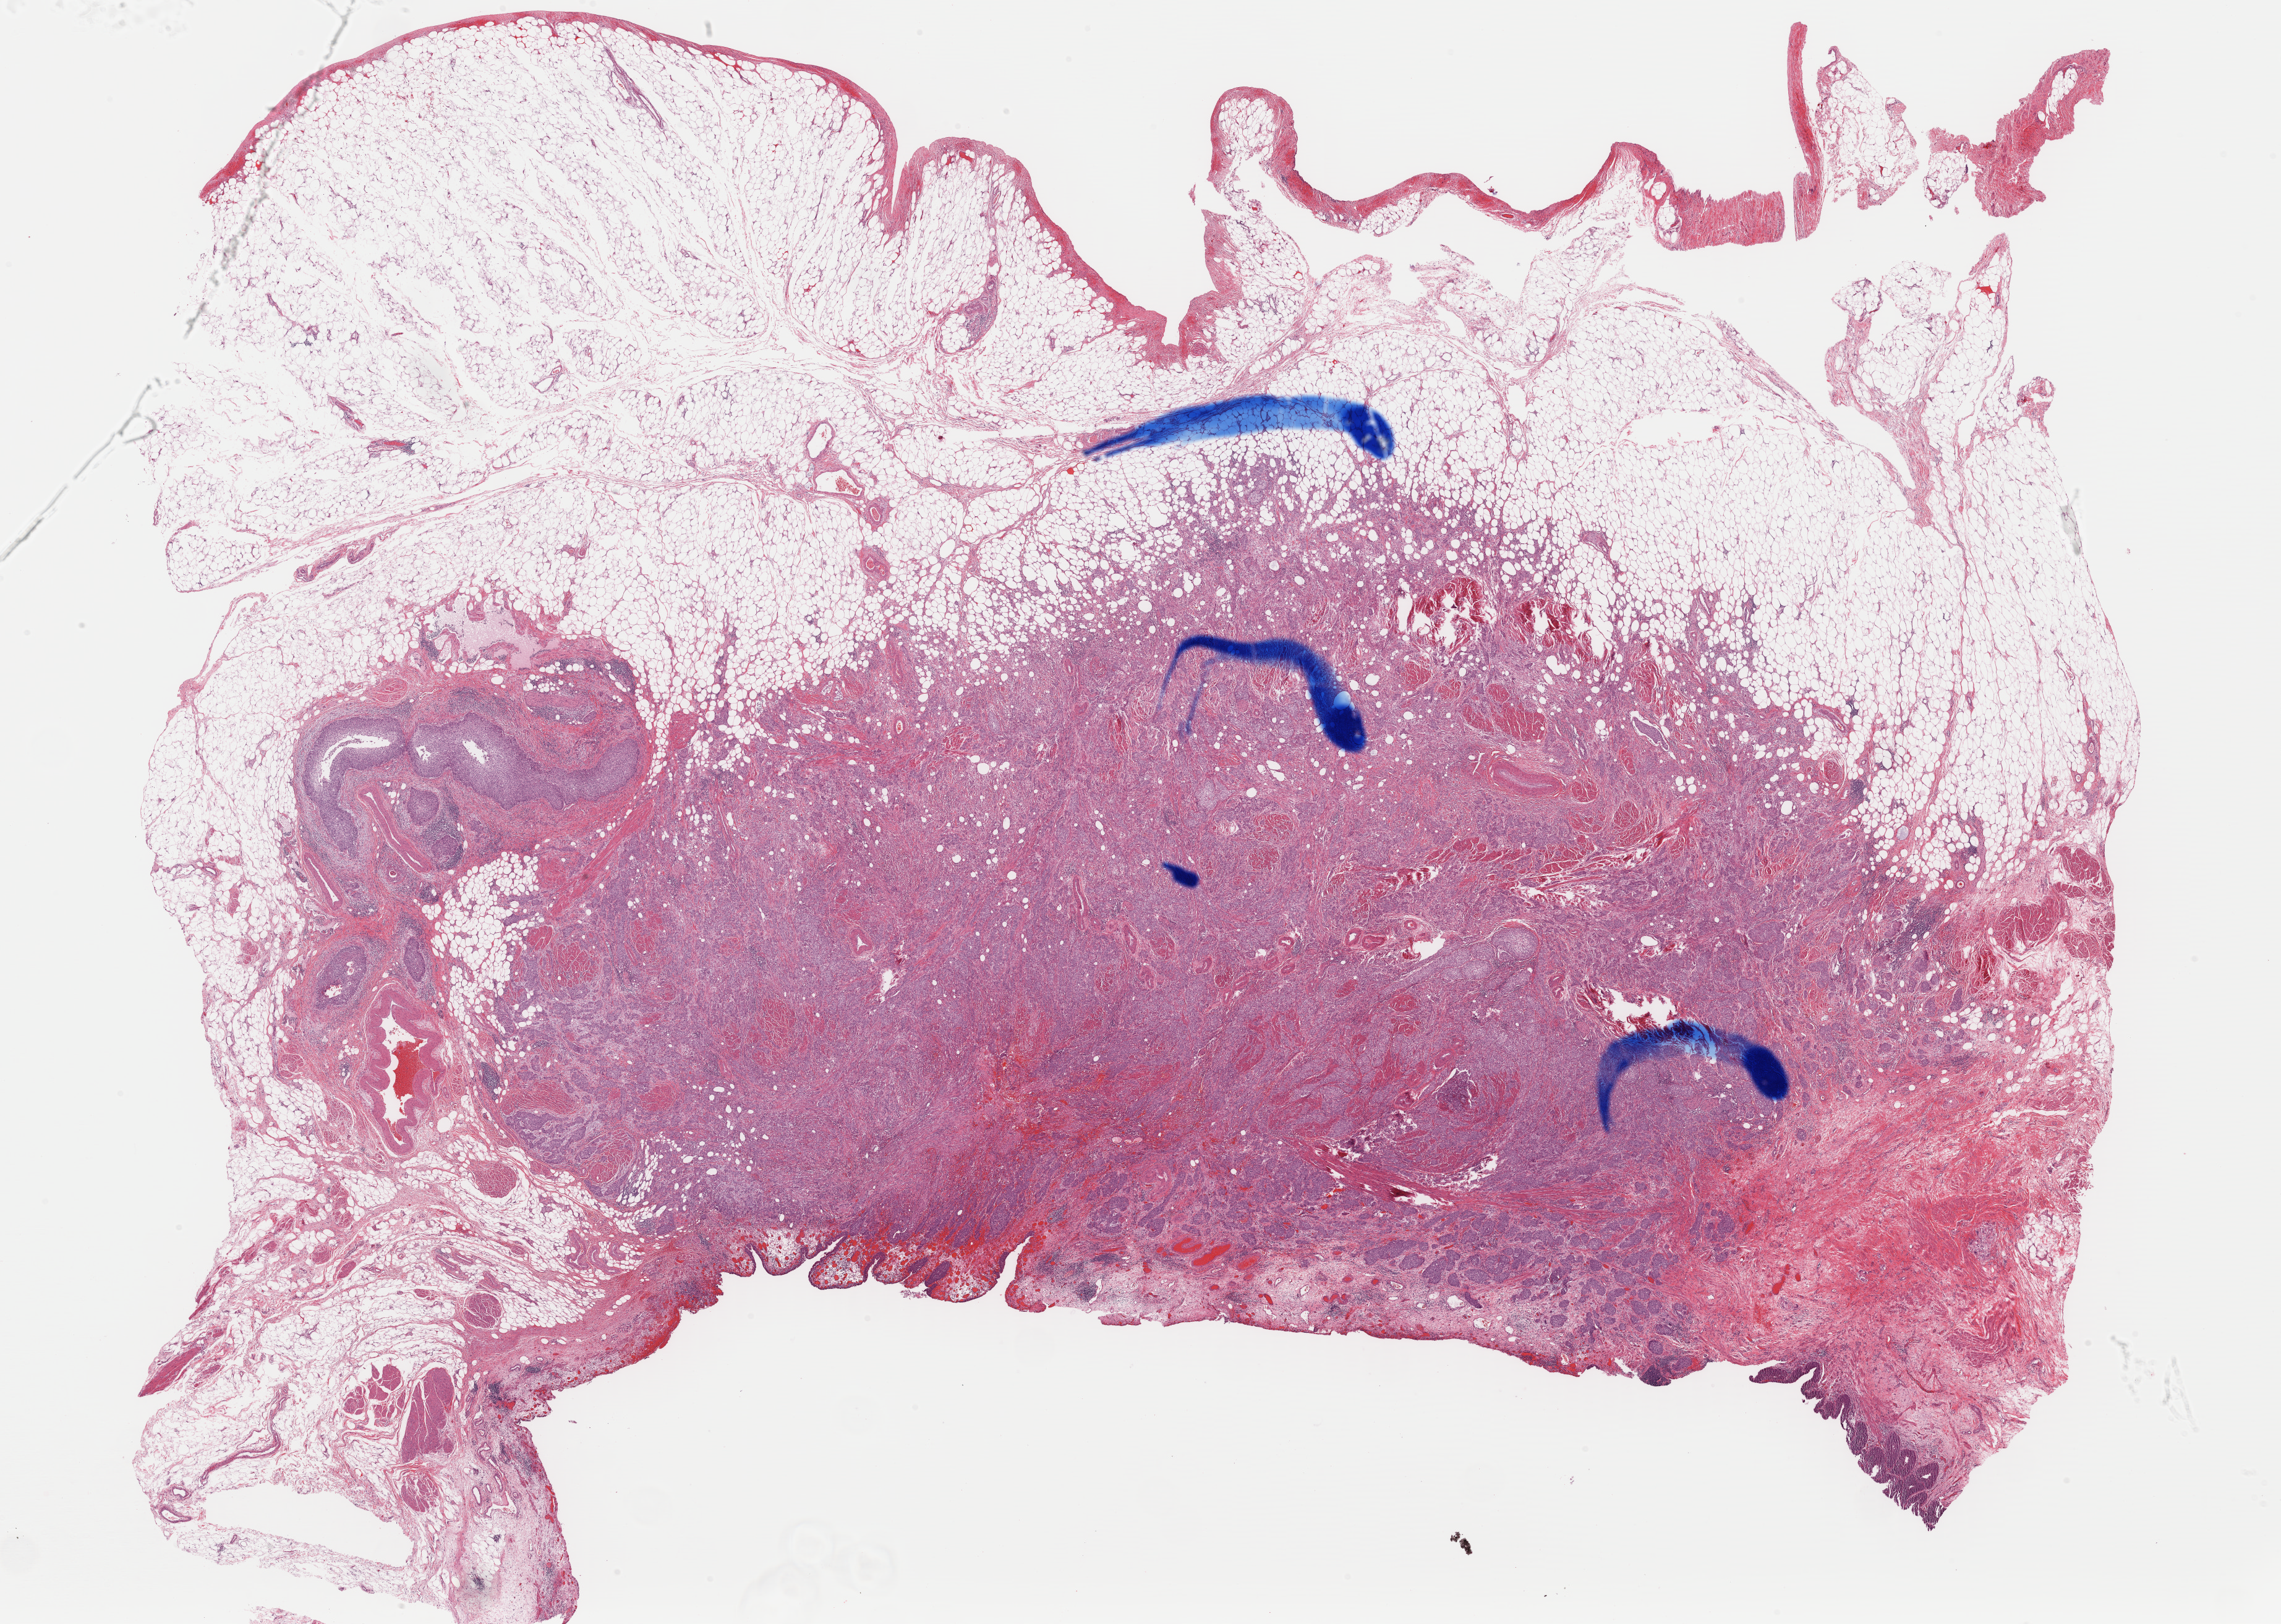
Whole-slide histology image, Hematoxylin and eosin (H&E) stained — low-resolution overview of the scanned area, about 29.1 x 20.7 mm (from a 40x scan), formalin-fixed paraffin-embedded (FFPE) diagnostic section, bladder, primary tumour sample. Female patient; age at initial diagnosis 73 years. Histologic grade: high grade.
AJCC pathologic stage: III (7th edition). TNM: T3a N0 M0. Pathologic diagnosis: Transitional cell carcinoma (dome of bladder).